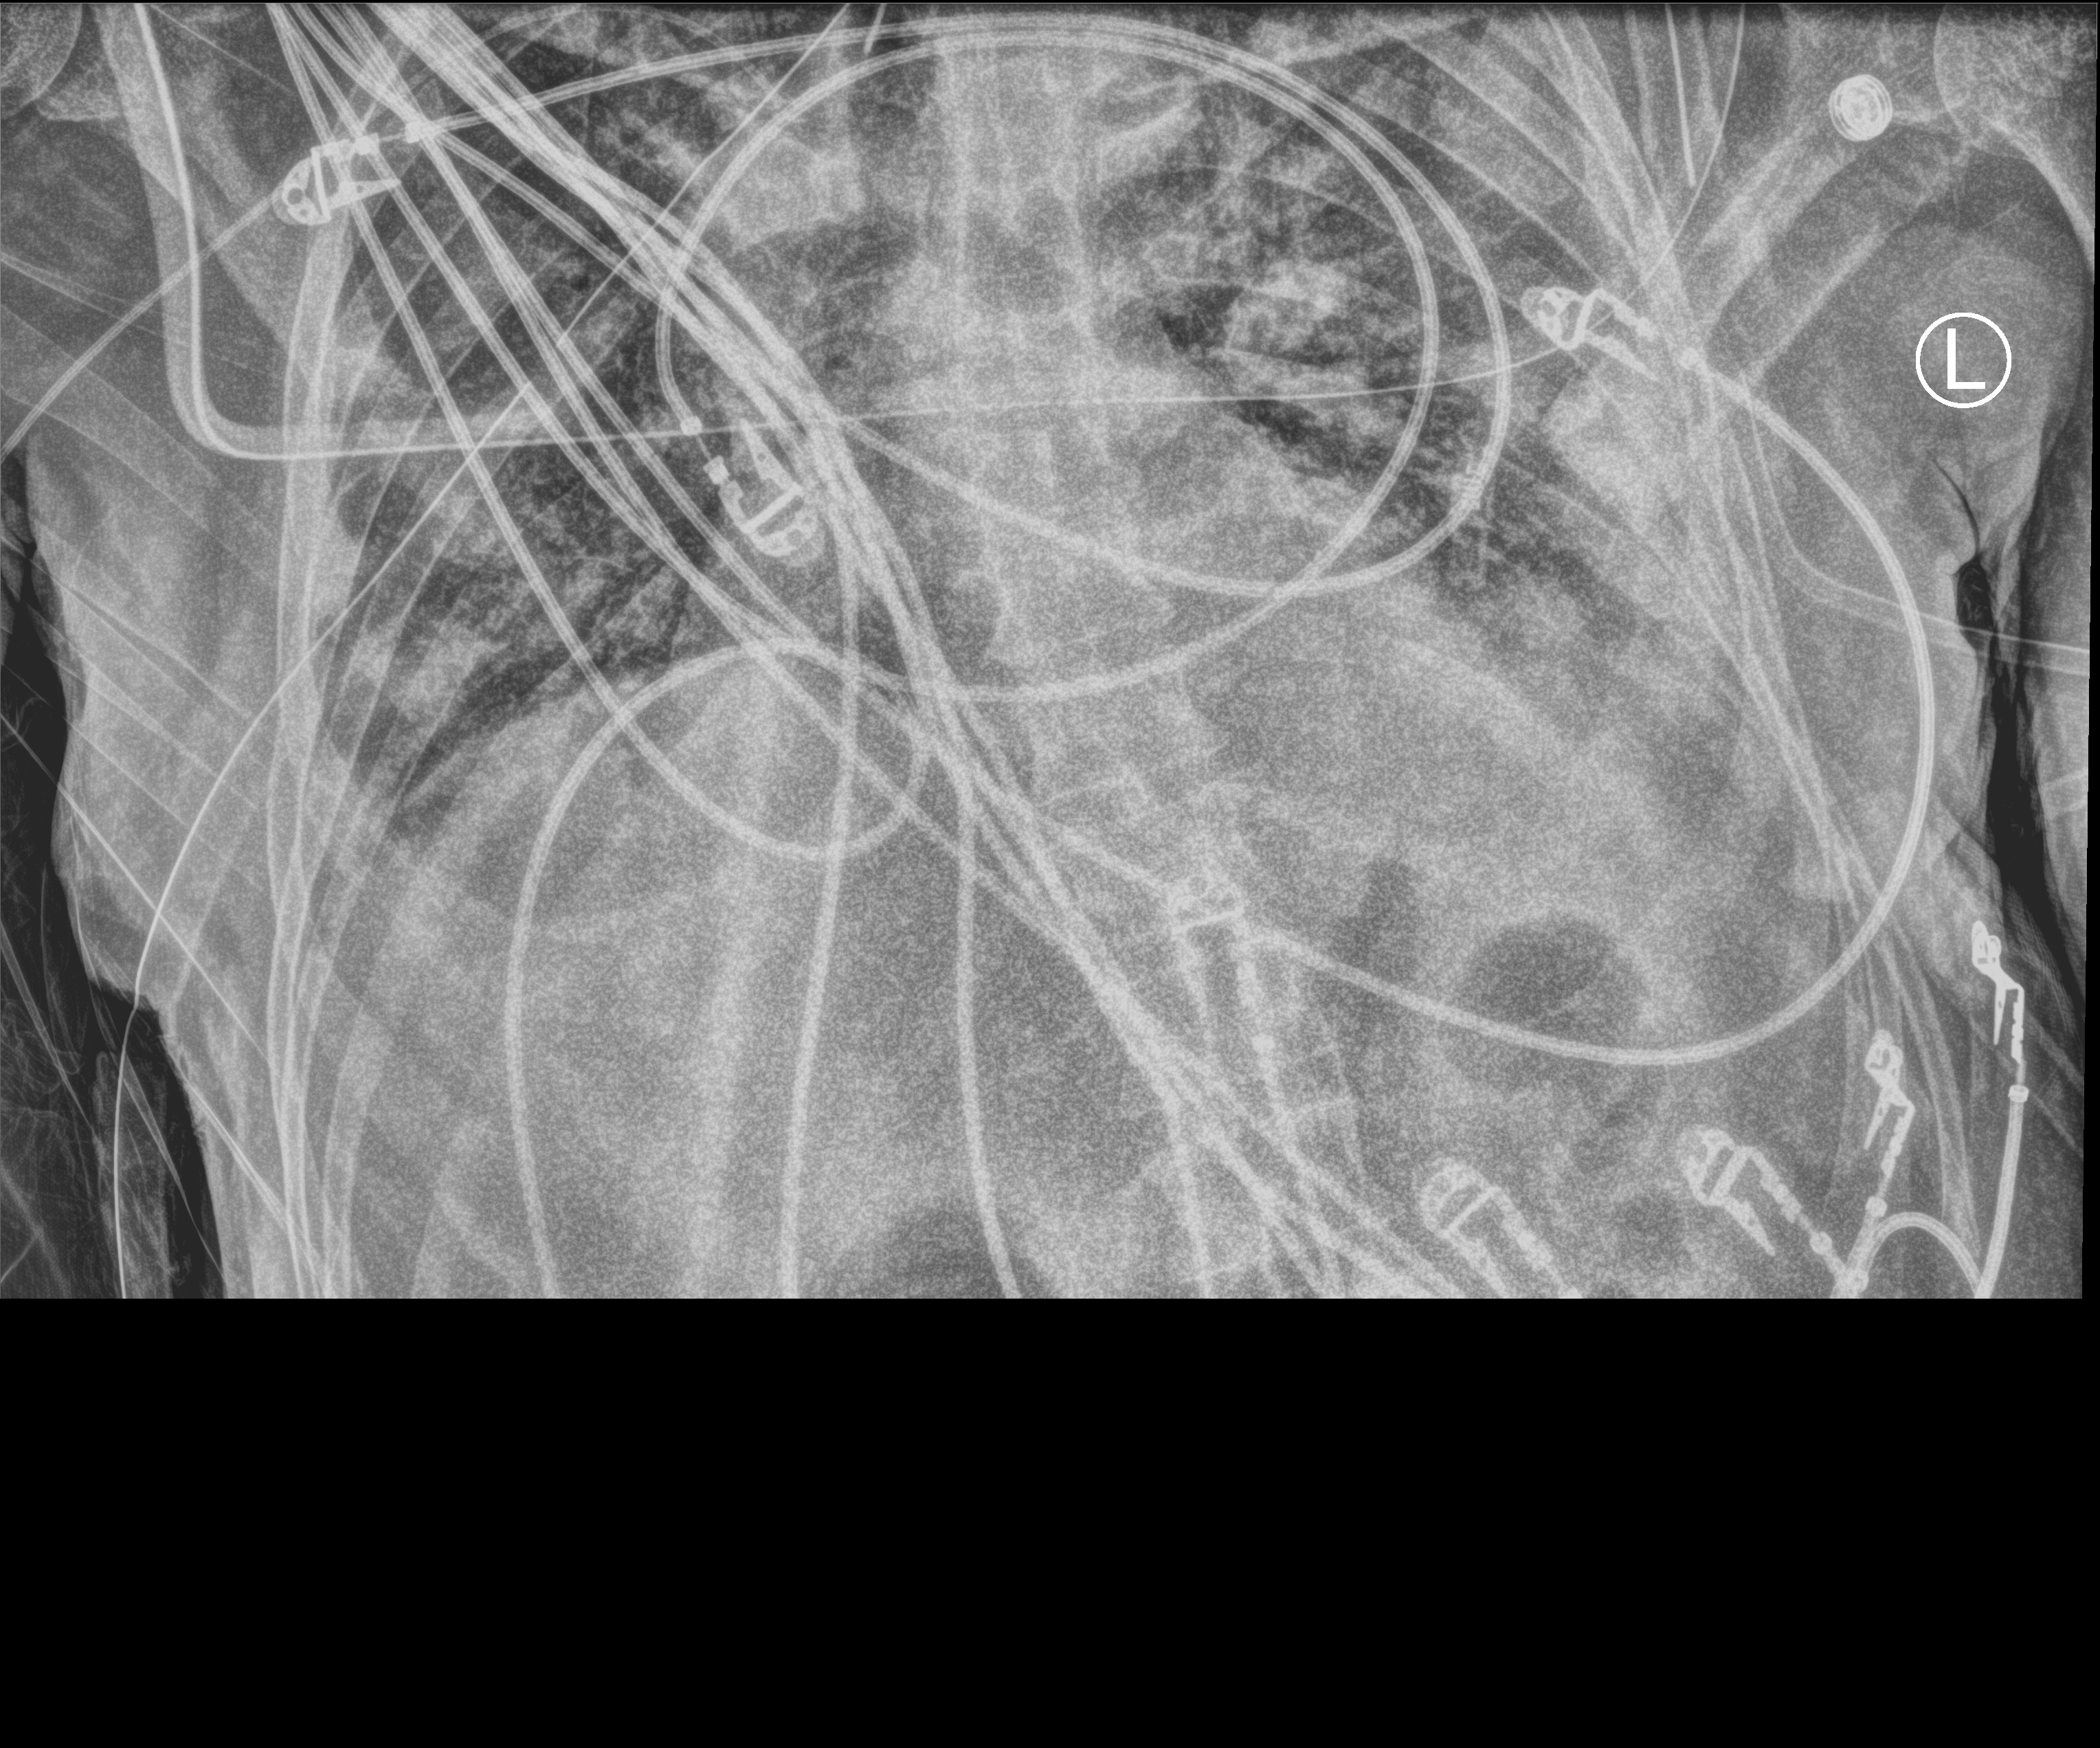
Portable chest radiograph; anteroposterior (AP) projection. Male patient hospitalised with COVID-19, age 18–59 years.
From the hospital-stay record, not from the radiograph (when in the stay this image was taken is not recorded):
- mechanically ventilated during this hospital stay: yes